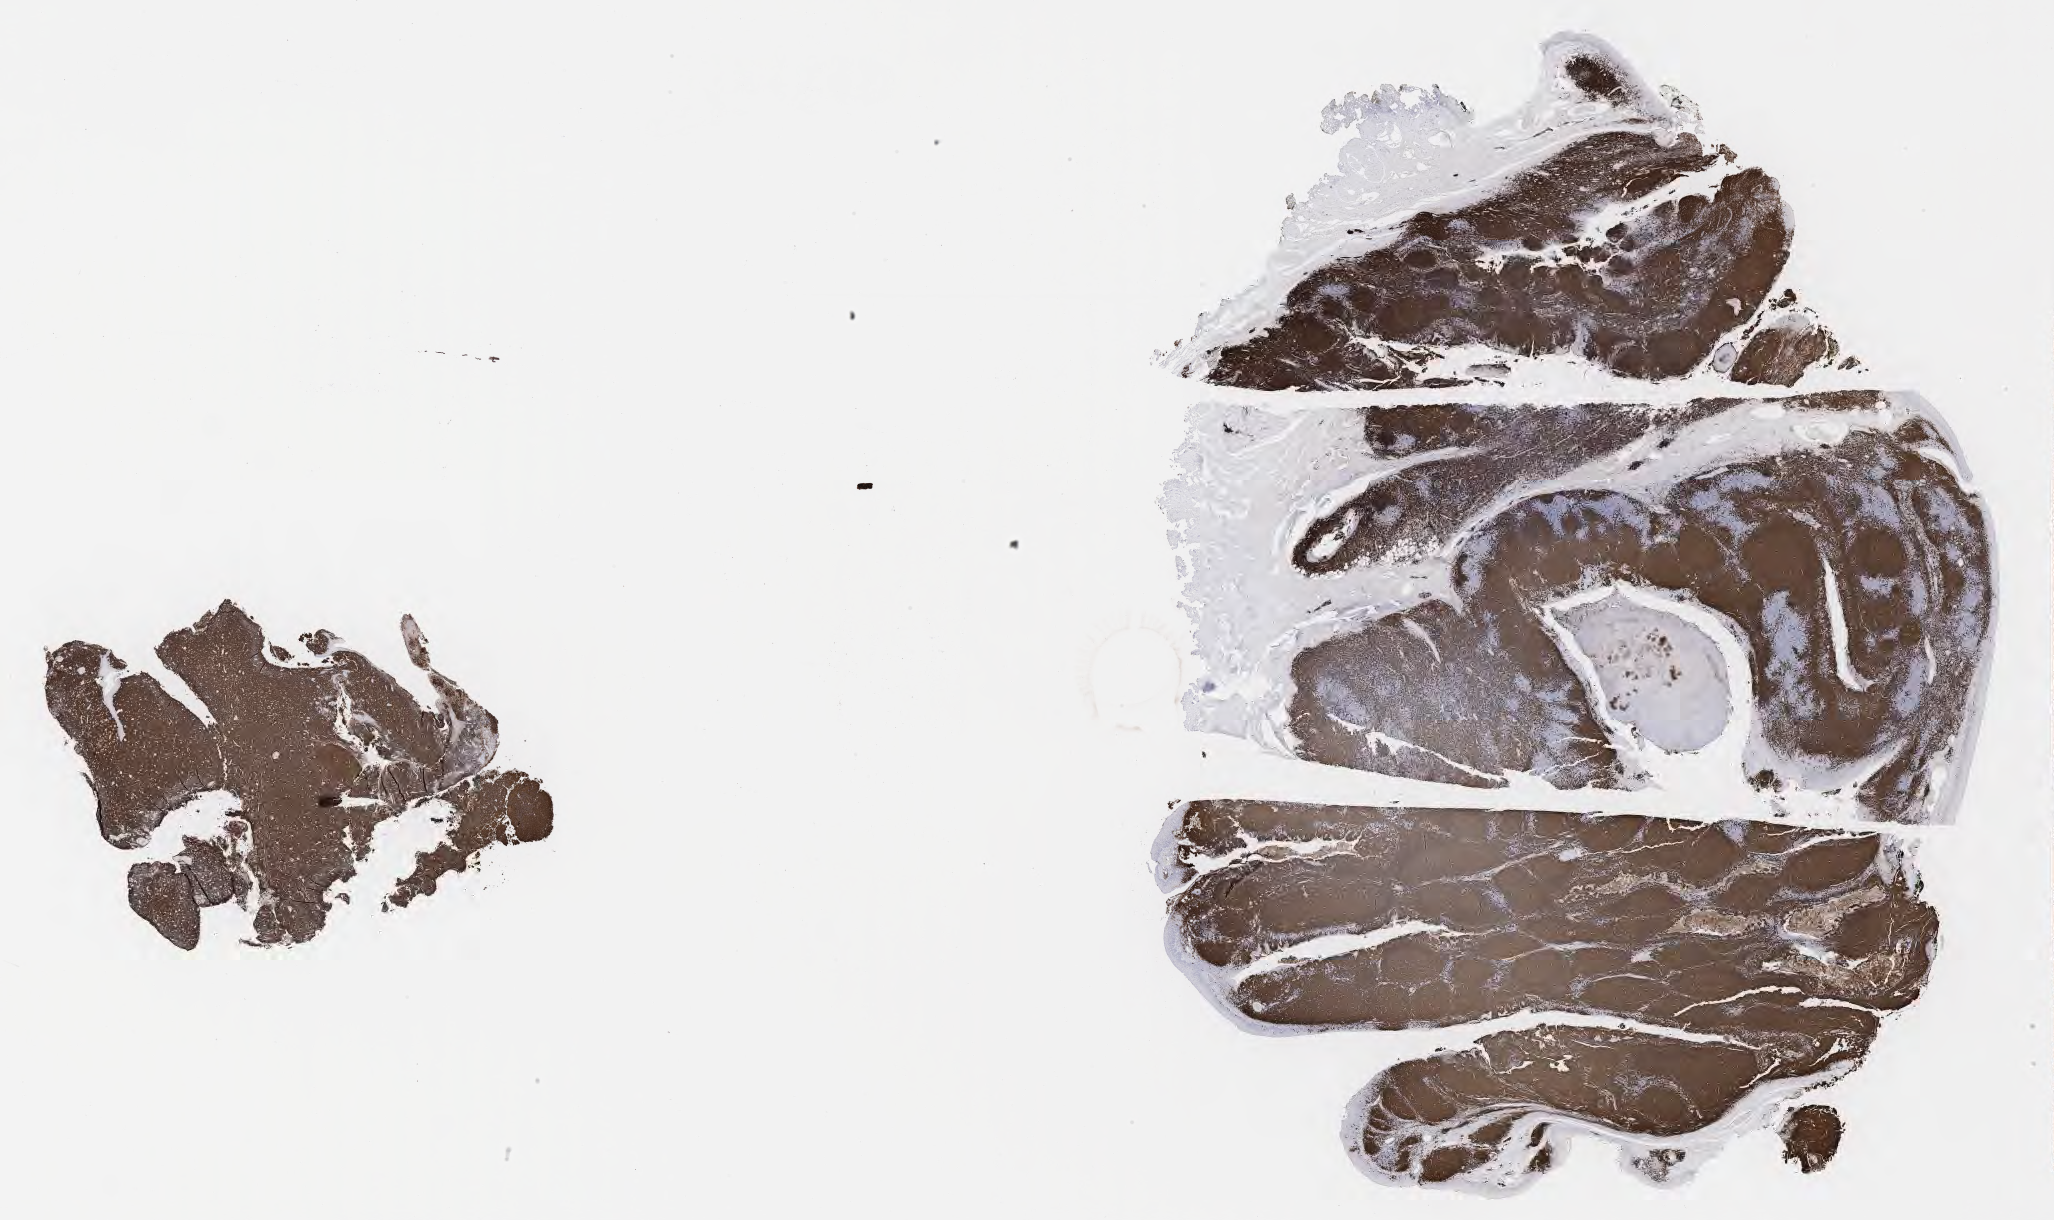
Immunohistochemistry (IHC) whole-slide image stained for CD20, whole scanned area (about 33.2 x 19.7 mm) shown as a low-resolution overview. Specimen: tumor tissue. Male patient; age at initial diagnosis 3 years.
* histologic diagnosis: Burkitt lymphoma, NOS